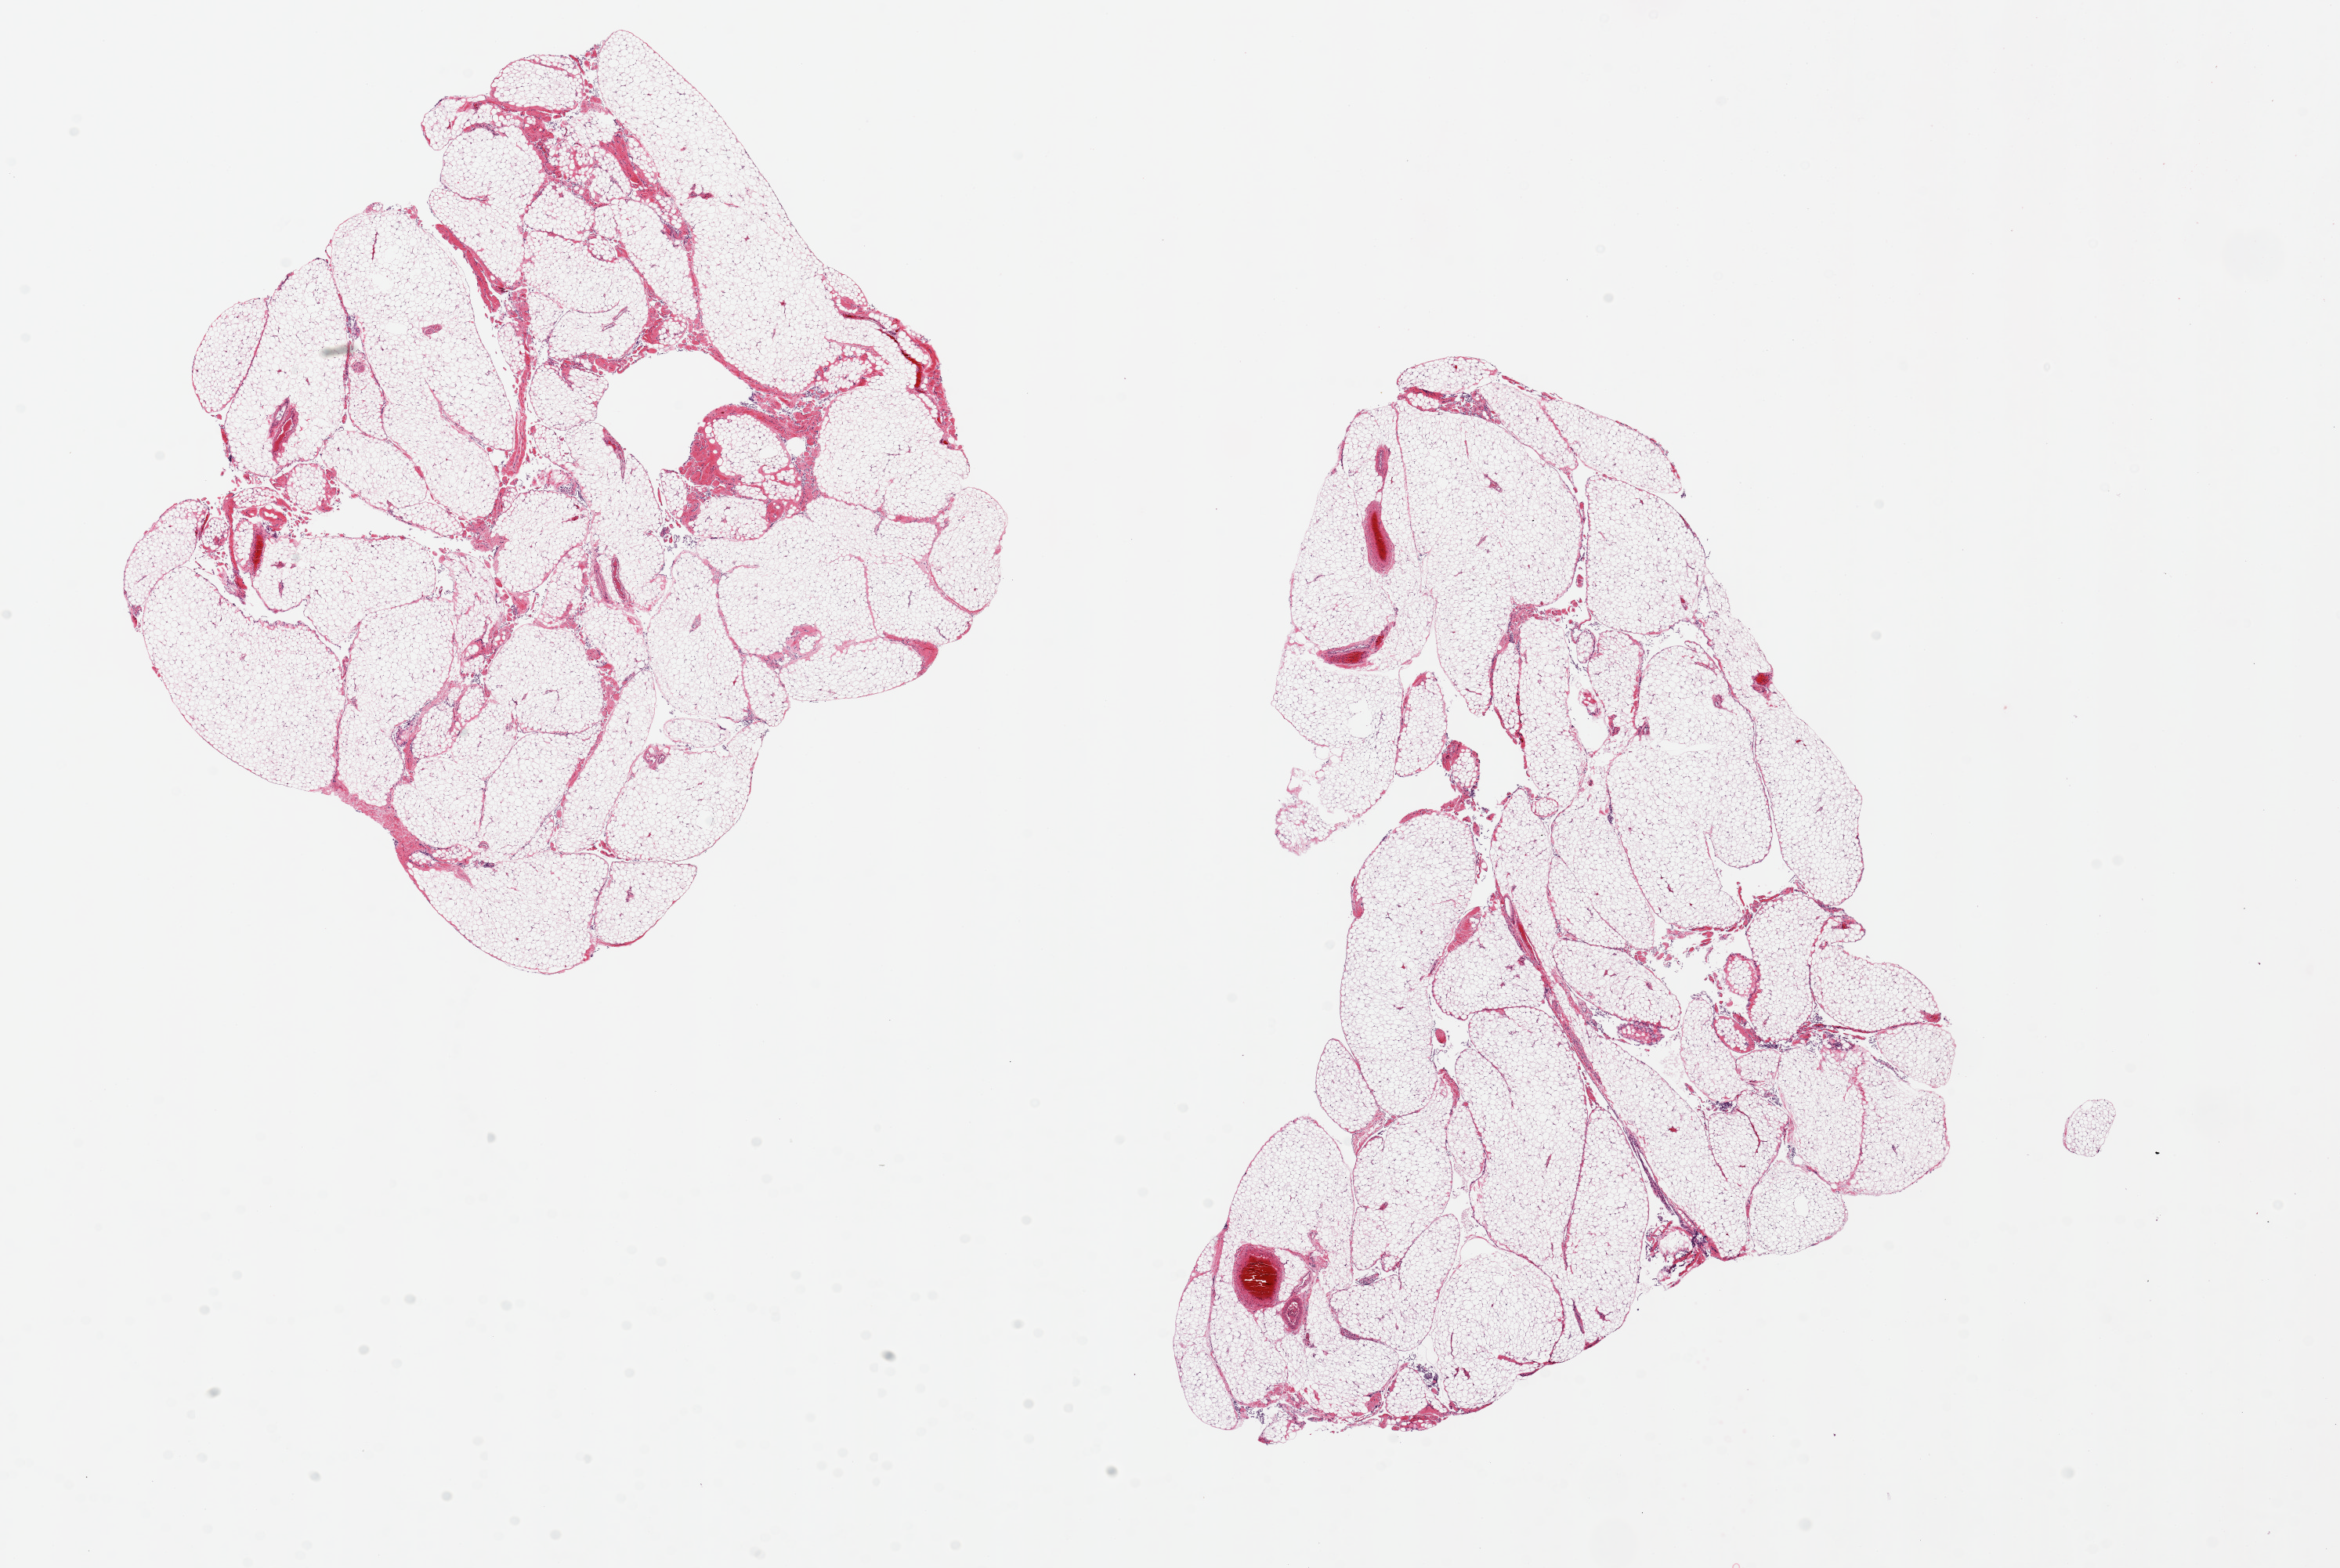
Whole-slide image, haematoxylin and eosin stain, a low-resolution overview of the entire scanned area, about 23.6 x 15.8 mm; PAXgene-fixed paraffin-embedded (PFPE) section; sampled site (target tissue): omentum; donor tissue sample.
Pathologist's review note for this sample: 2 pieces ~9x7mm.